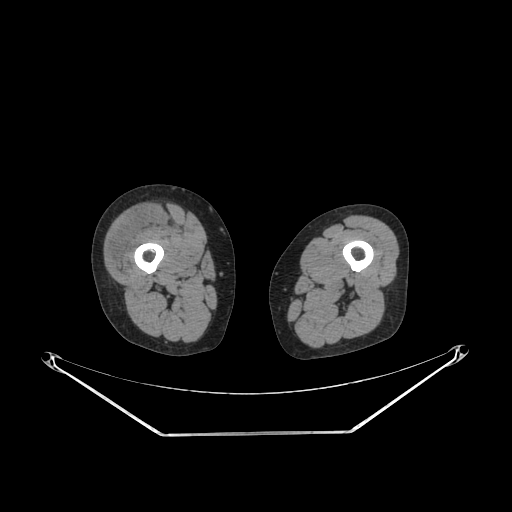
CT of an extremity soft-tissue mass (from a PET/CT study), one axial slice. Position 218 of 311 along the scan axis. Reconstruction kernel SOFT. 140 kVp. Soft-tissue window (W 400 / L 40 HU). 3.75 mm slice thickness. 512 × 512 image matrix, field of view 500 × 500 mm. Female patient. From the clinical record (not read from this slice): histological type: pleiomorphic undifferentiated sarcoma; grade: high; site of the primary tumour: right quadricep.
Outlined on this slice (expert contour drawn on MRI and transferred to this co-registered scan by the dataset authors):
- tumour plus oedema (research contour): bounding box (x1, y1, x2, y2) in pixels: (107, 208, 163, 270)